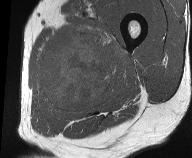
MRI of an extremity soft-tissue mass, one axial slice. Position 21 of 61 along the scan axis. MR volume resampled by the dataset authors to the PET/CT grid (not the native acquisition matrix). 192 × 158 image matrix, field of view 187 × 154 mm. Male patient. Case-level facts recorded for this patient, not image findings: histological type: pleiomorphic liposarcoma; grade: high; site of the primary tumour: left thigh.
Outlined on this slice (expert contour drawn on MRI and transferred to this co-registered scan by the dataset authors):
- gross tumour volume including surrounding oedema: bounding box <36,23,128,118> (left, top, right, bottom; pixels)
- gross tumour volume (mass): <38,34,113,111>